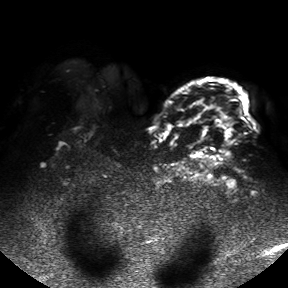
Breast MRI, one axial slice. Position 35 of 50 along the scan axis. Diffusion-weighted series; image 2 of 4 stored at this slice position (different b-values; order by instance number). 1.5 T. 4 mm slice thickness. 288 × 288 image matrix, field of view 390 × 390 mm. Female patient.
Annotated regions visible in this slice (manually delineated by an expert):
- tumour on diffusion-weighted imaging: bounding box [x1, y1, x2, y2] px = [222, 117, 232, 139]